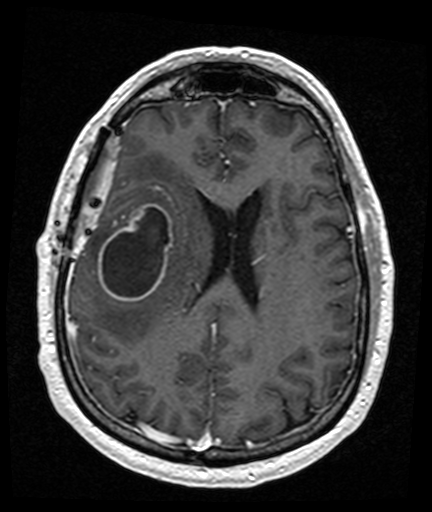
Brain MRI from a brain-tumour surgery series, one axial slice. Slice 63 of 176 in the series (ordered by position). T1-weighted post-contrast. 1 mm slice thickness. 432 × 512 image matrix, field of view 194 × 230 mm. From the clinical record (not read from this slice): histopathology: Glioblastoma; WHO grade: 4; IDH mutation: no.
Outlined on this slice (outlined manually by an expert reader):
- tumour: bounding box [x1, y1, x2, y2] px = [99, 204, 173, 302]